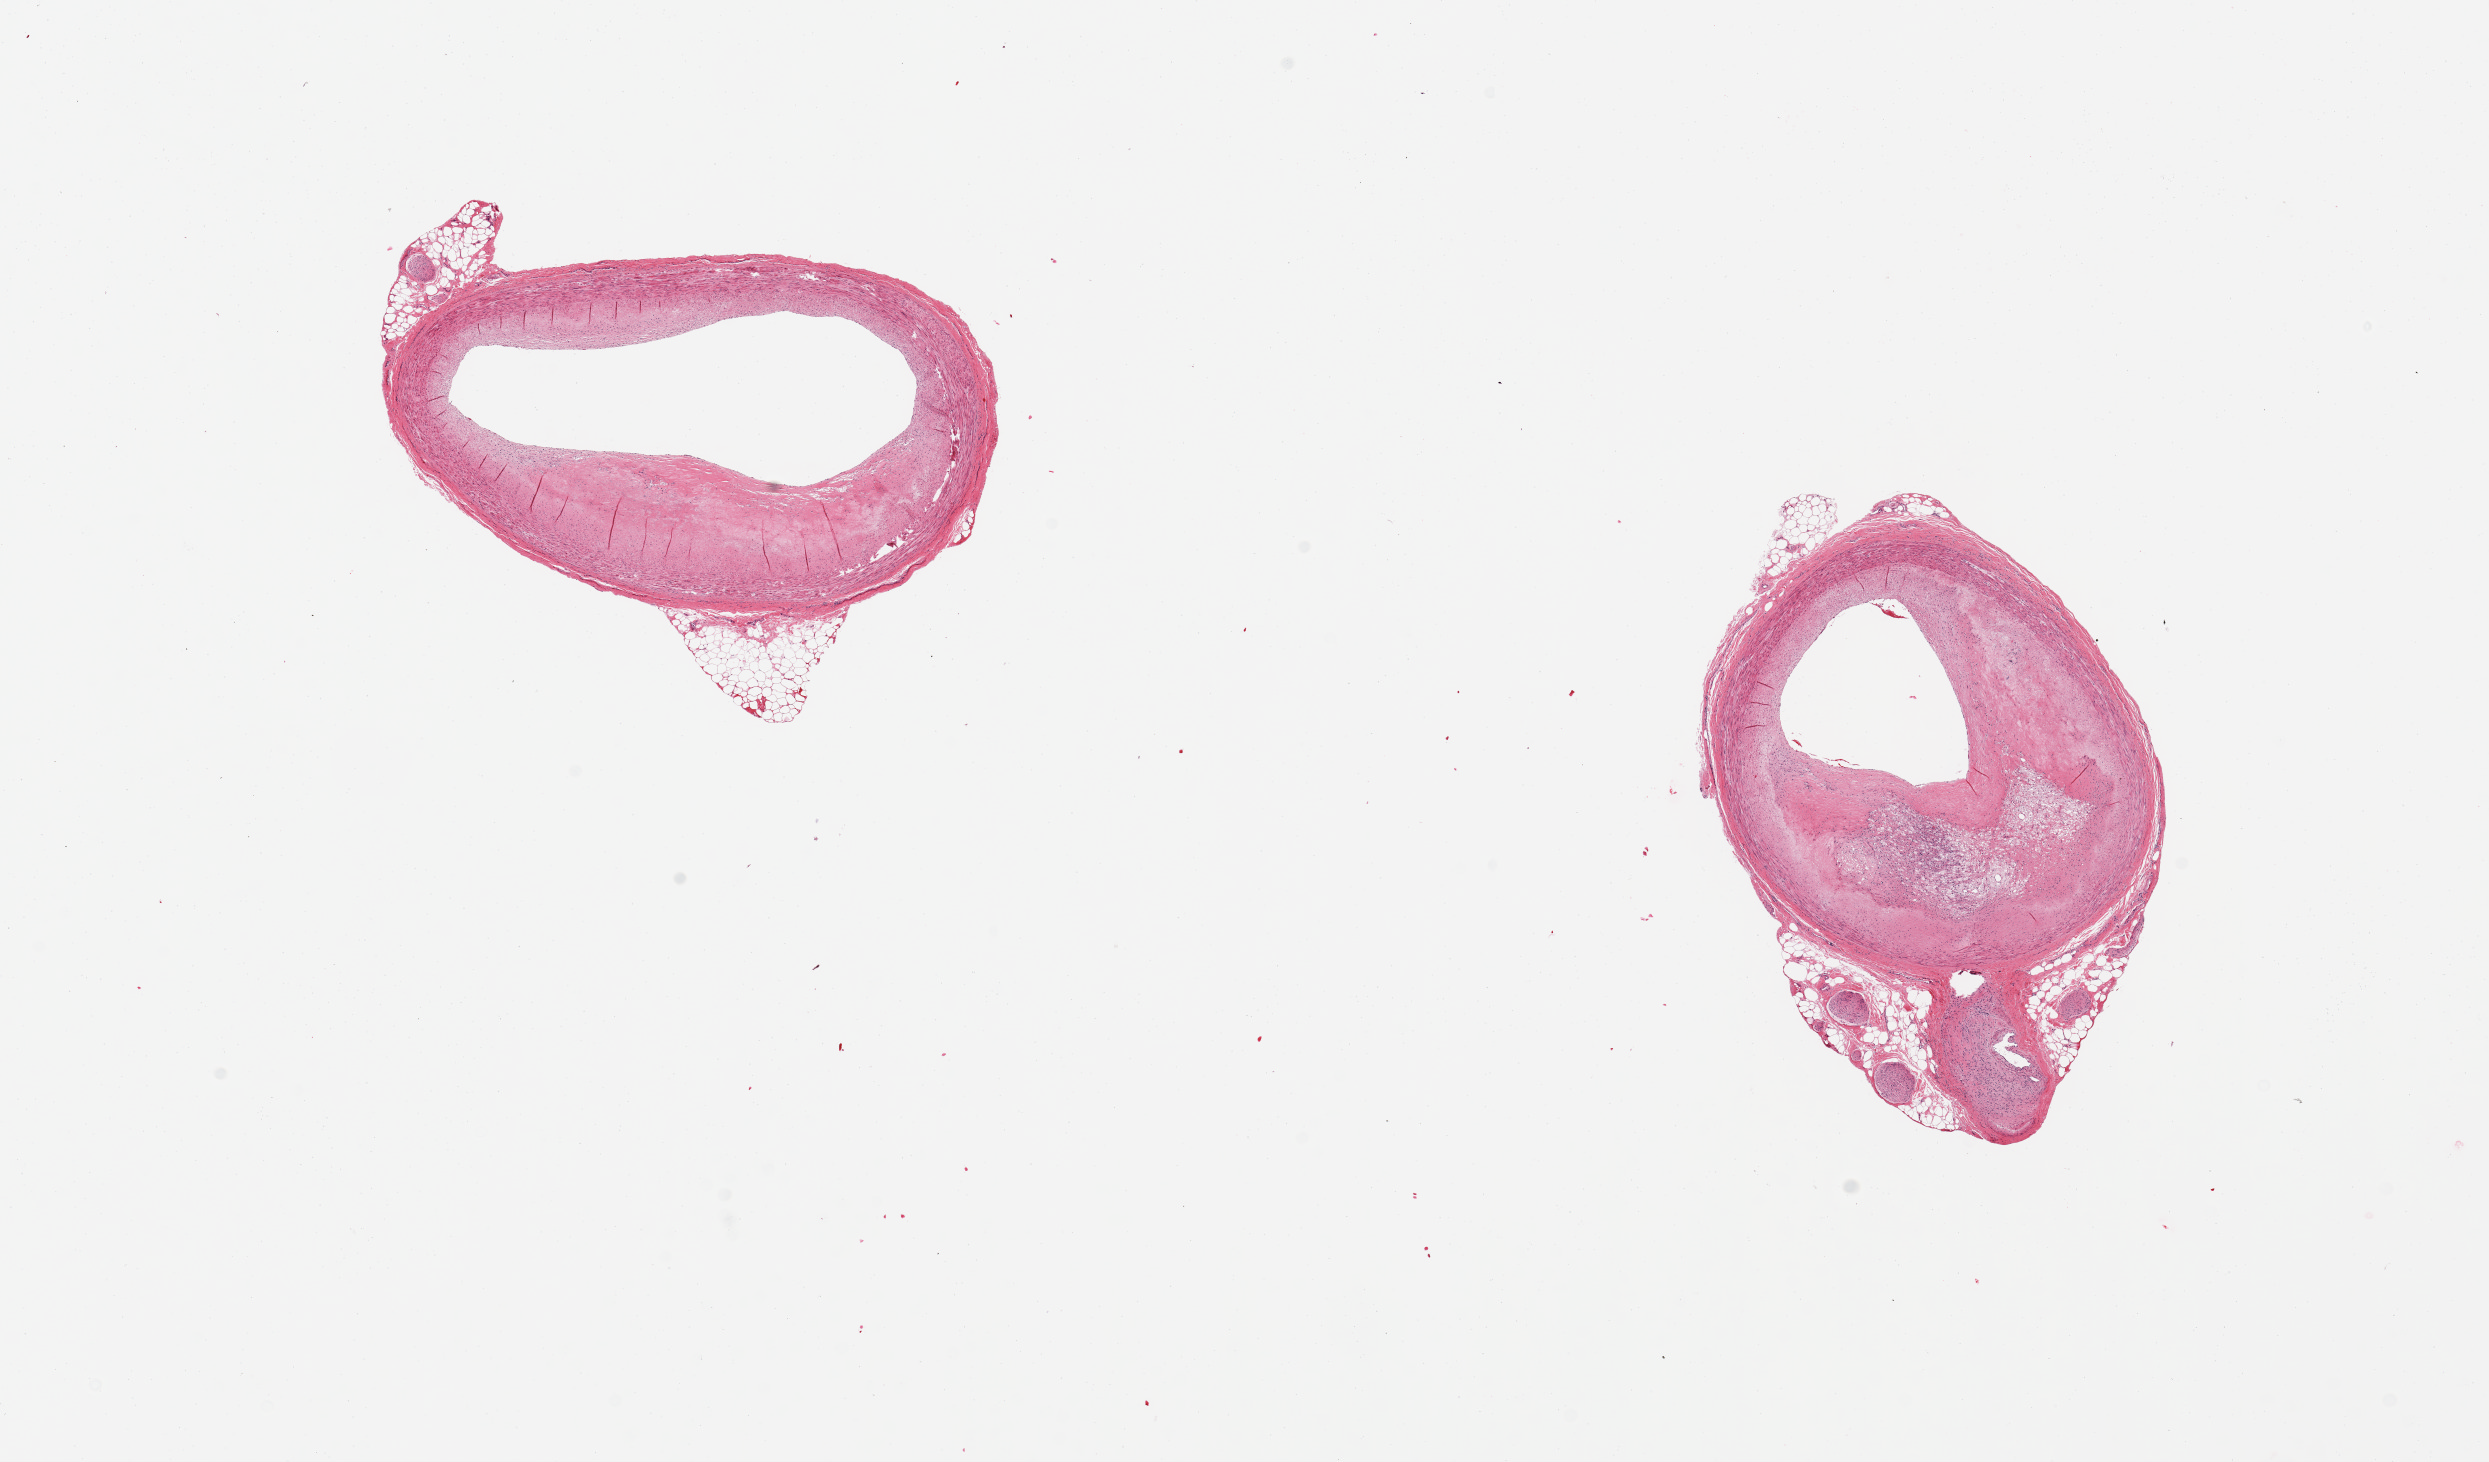
Whole-slide image, hematoxylin and eosin (H&E) stain, brightfield, shown as a low-resolution overview of the whole scanned area (about 19.7 x 11.6 mm). PAXgene-fixed paraffin-embedded (PFPE) section. Sampled site (target tissue): coronary artery. Tissue donor sample.
Review note (as recorded): 2 pieces; eccentric atheromatous plaque up yo 1.3 mm thick; 10% external fat.